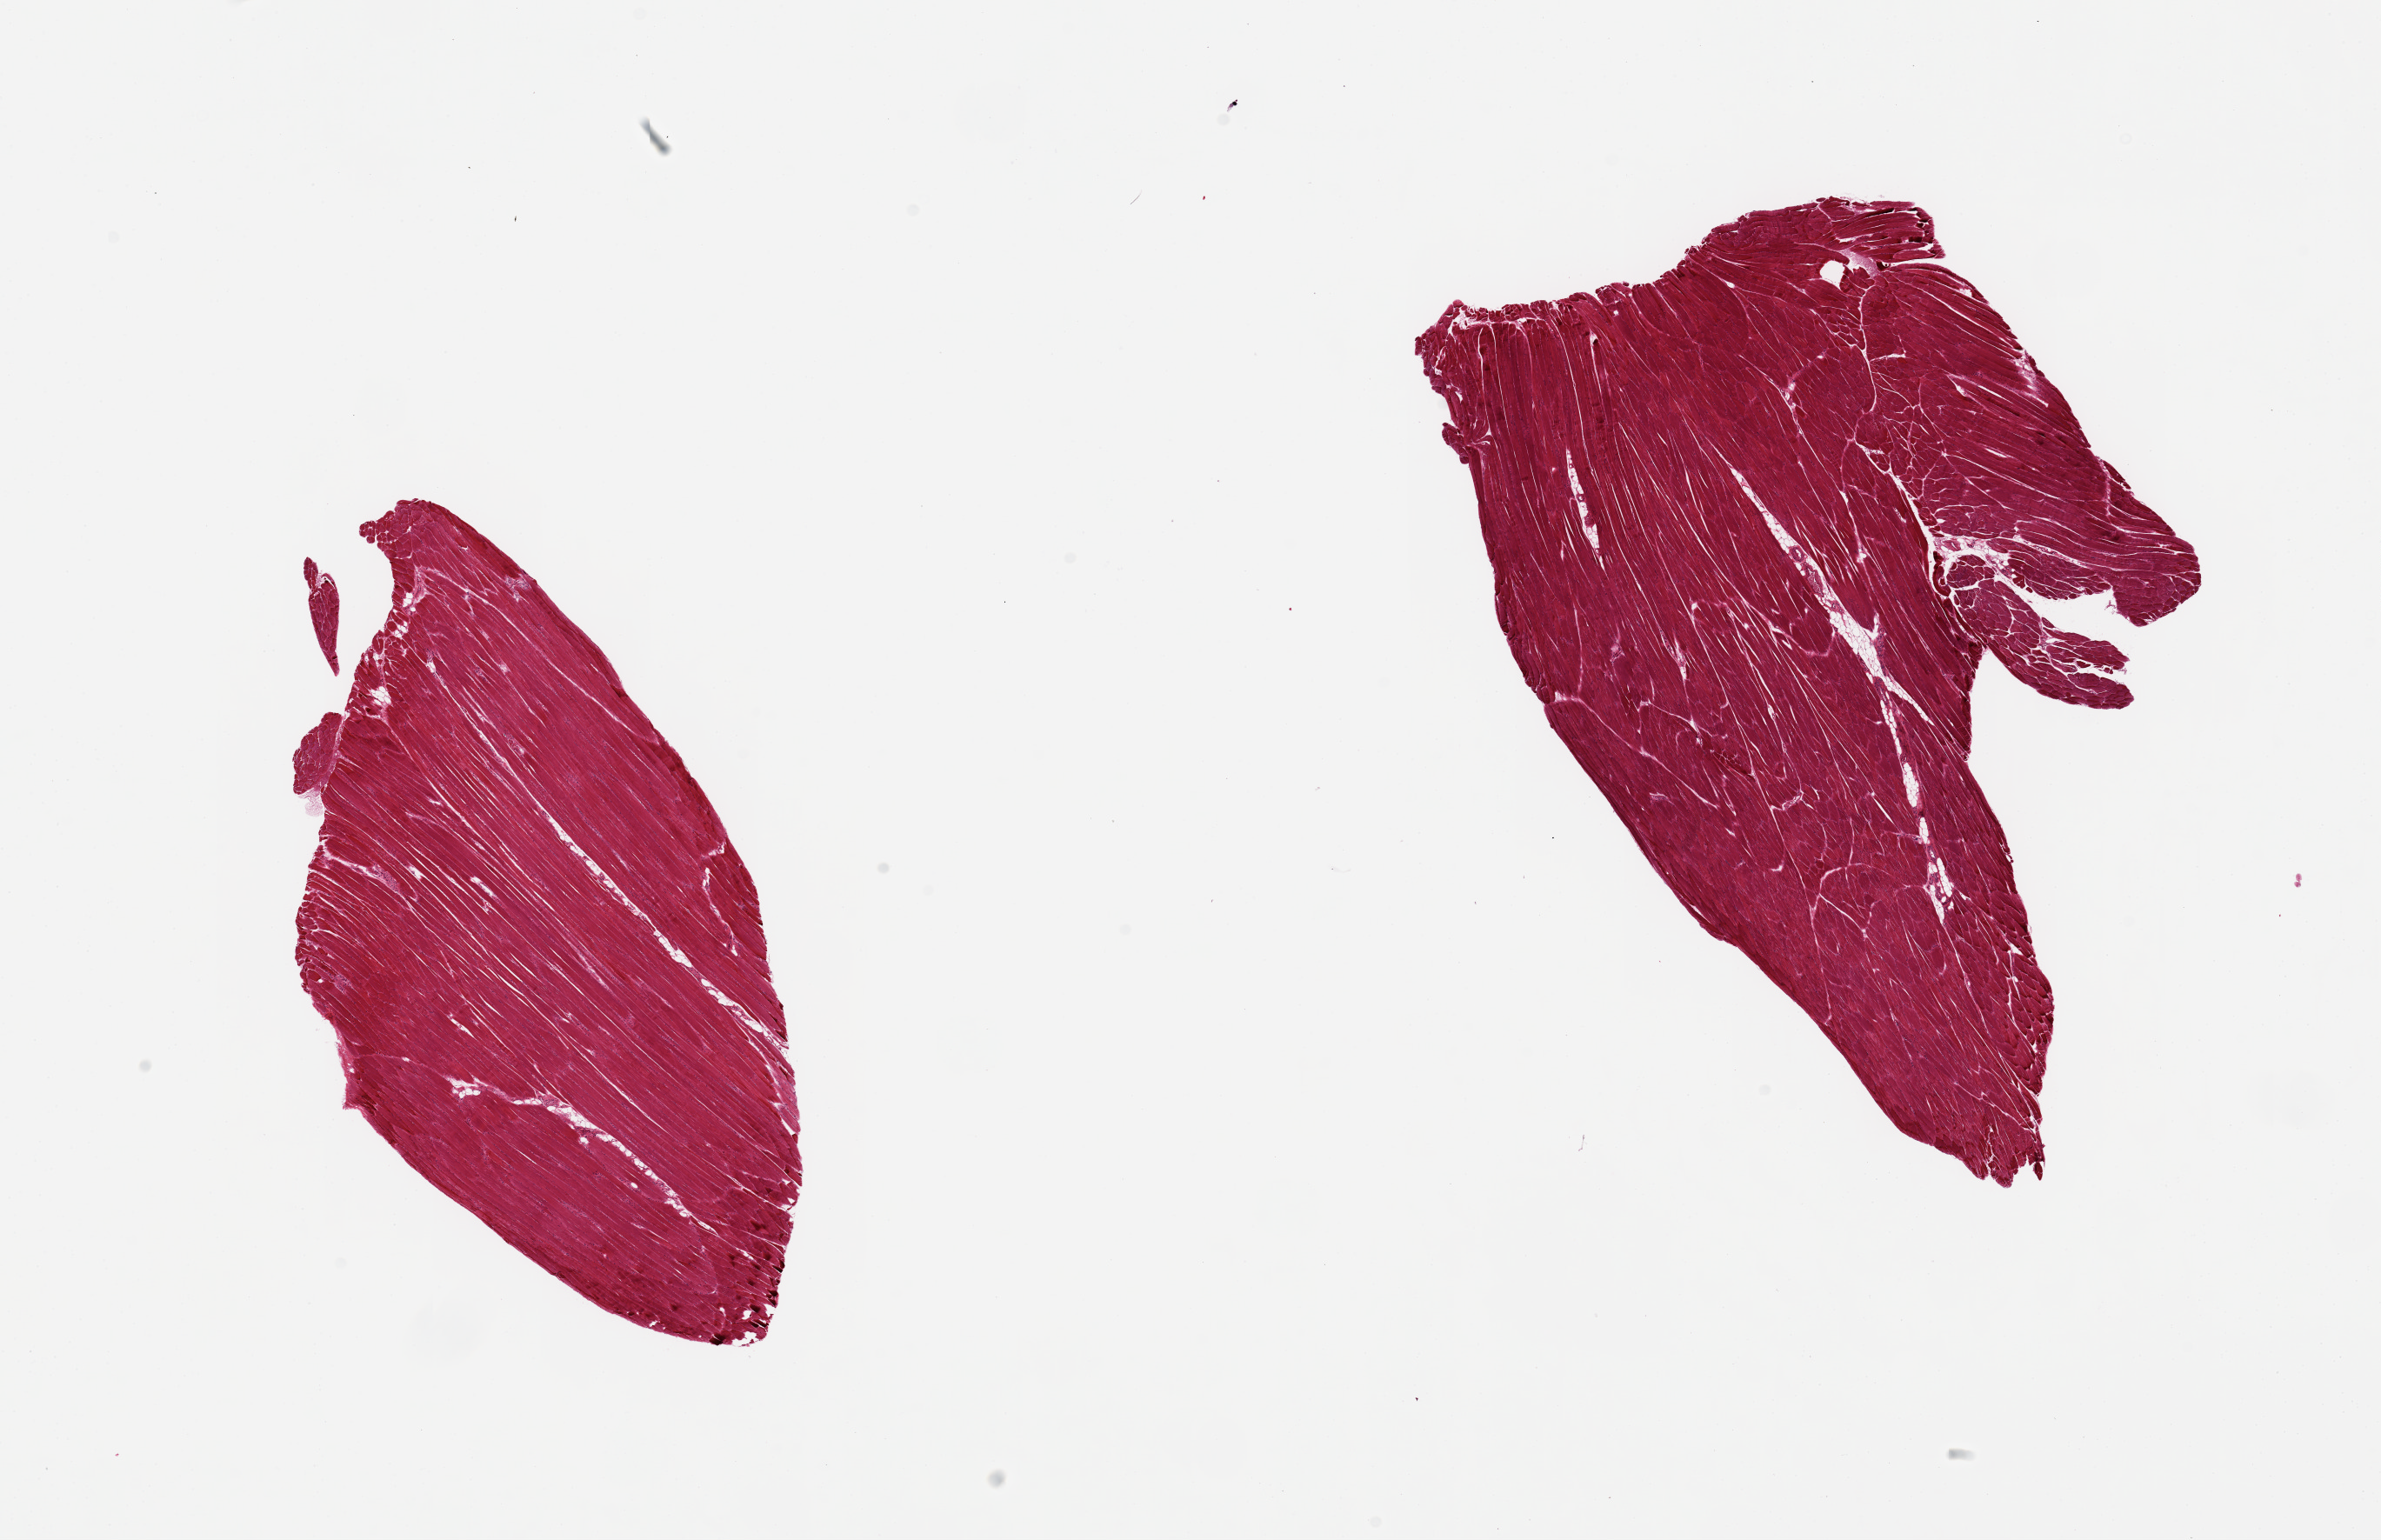
Digitized hematoxylin and eosin (H&E)-stained section, brightfield, shown as a low-resolution overview of the whole scanned area (about 21.7 x 14.0 mm, acquisition: 20x scan); PAXgene-fixed, paraffin-embedded tissue; section of skeletal muscle (target tissue); donor tissue sample. Donor sex: male.
Reviewer comment on this tissue sample: 2 pieces; minimal internal fat.